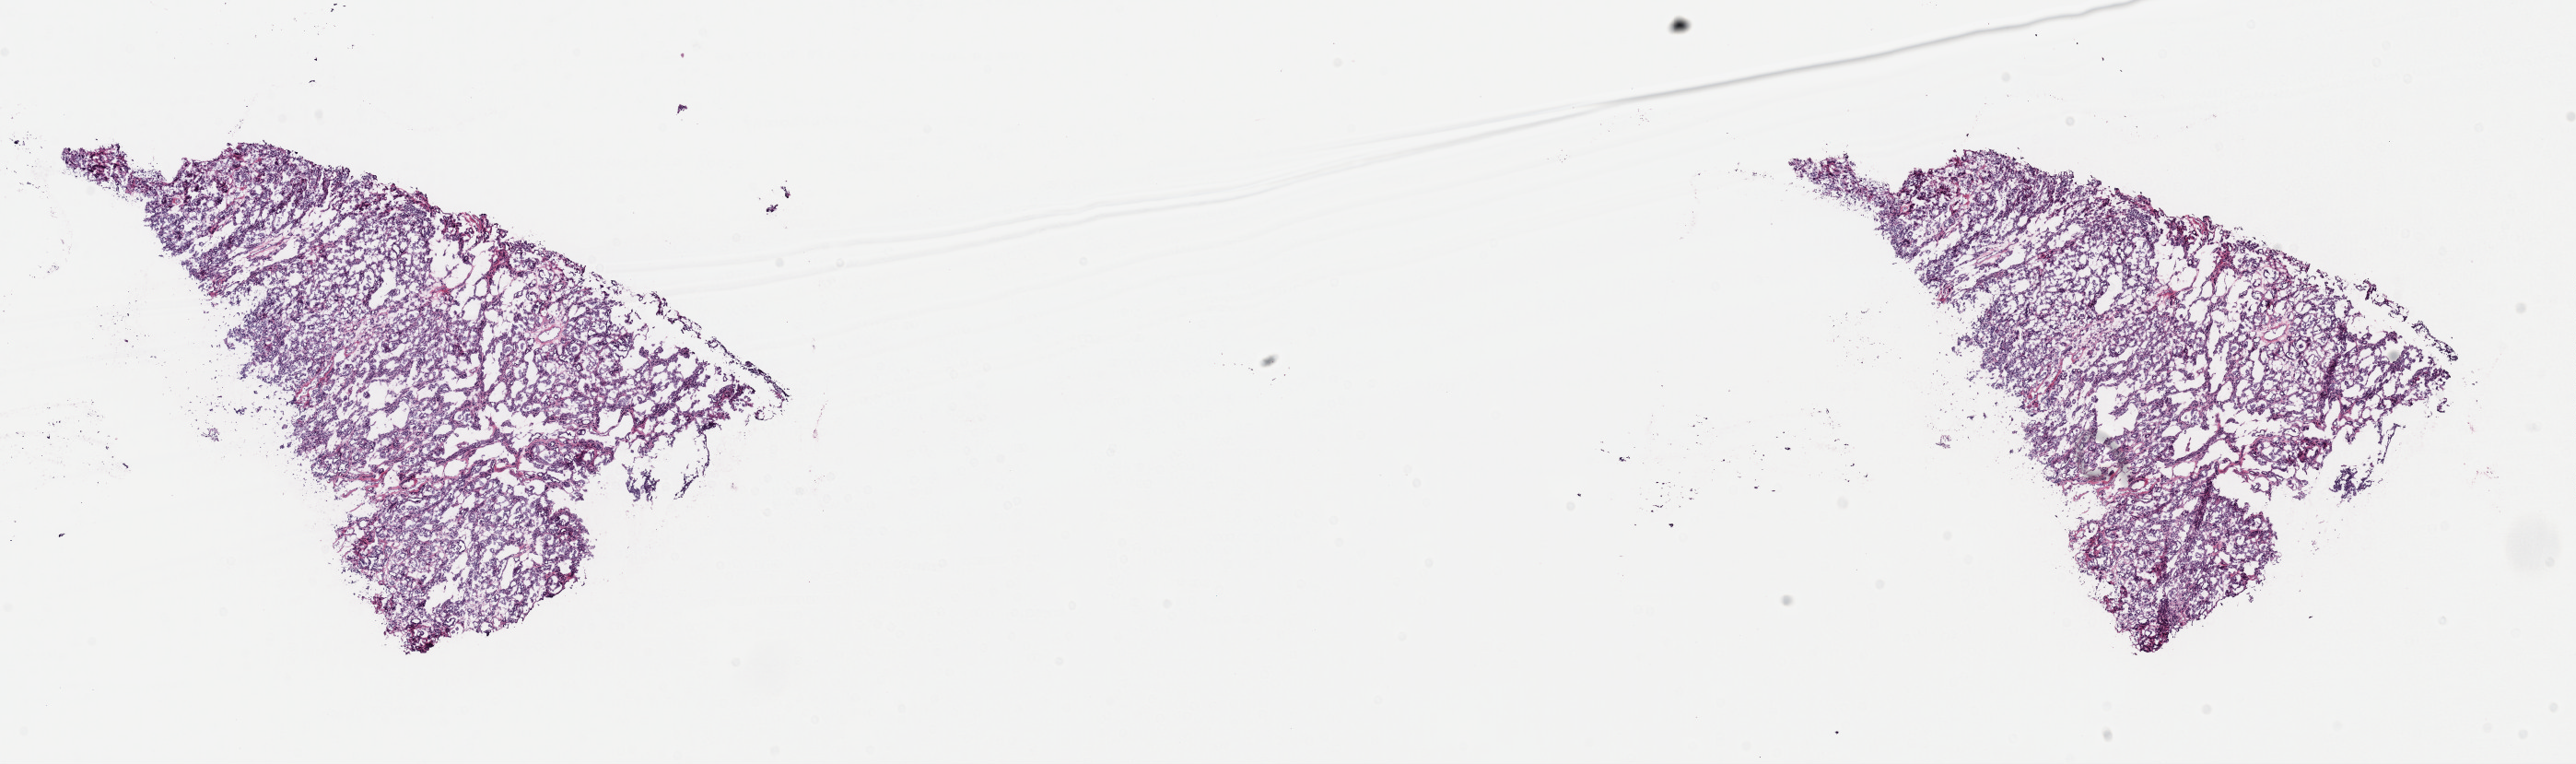
Hematoxylin and eosin (H&E) stained whole-slide image — whole scanned area (about 22.1 x 6.5 mm, acquisition: 40x scan) shown as a low-resolution overview; frozen section from the top of the tissue portion; sample: primary tumour, thyroid. Female, age 80 years at initial diagnosis. Pathologist review of this section (percent, as recorded): tumour cells 80%, tumour nuclei 80%, normal cells 0%, stromal cells 20%, necrosis 0%. Infiltration values recorded for this section: lymphocyte infiltration 0%, monocyte infiltration 0%, neutrophil infiltration 0%.
Laterality: bilateral. AJCC pathologic stage: III (7th edition). Diagnosis: Papillary adenocarcinoma, NOS (thyroid gland).